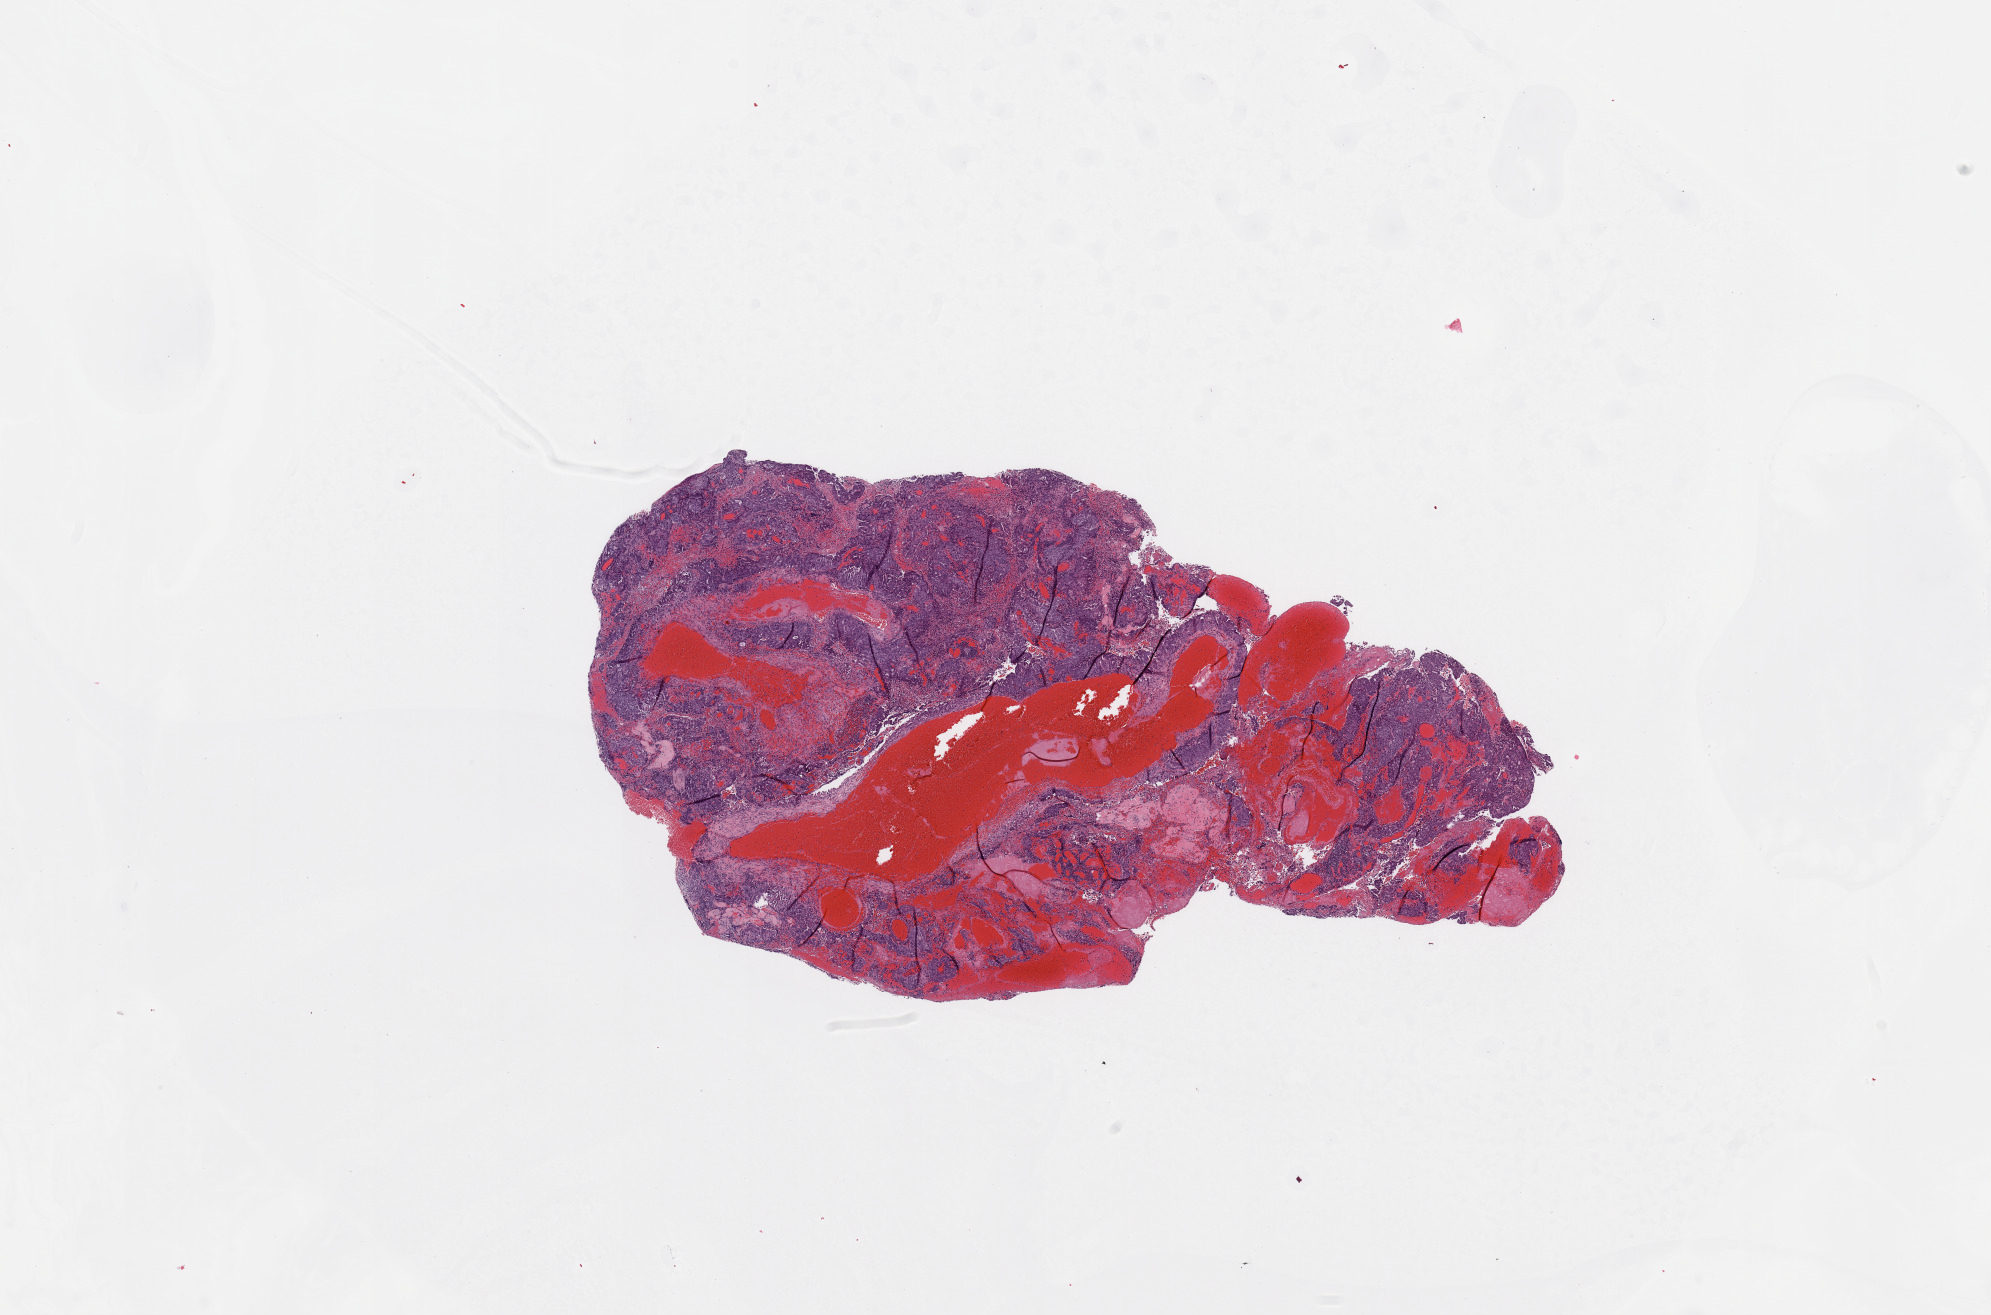
Whole-slide histology image, Hematoxylin and eosin (H&E) stained, a low-resolution overview of the entire scanned area, about 15.8 x 10.4 mm; tumour tissue sample, uterus. 48-year-old female patient. Histologic grade: G3 (poorly differentiated).
AJCC pathologic stage: II. Histologic diagnosis: Endometrioid adenocarcinoma, NOS.